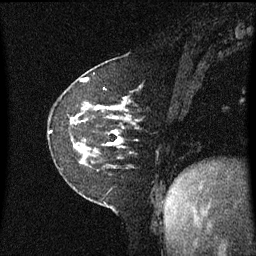
Breast MRI (dynamic contrast-enhanced), one sagittal slice; position 20 of 60 along the scan axis; dynamic contrast-enhanced series, image 2 of 3 at this slice position (ordered by acquisition); 1.5 T; TE 4.2 ms, TR 8.4 ms; 2 mm slice thickness; 256 × 256 image matrix, field of view 210 × 210 mm. Patient: female, 60 years. Case-level facts recorded for this patient, not image findings: setting: breast cancer imaged before/during neoadjuvant chemotherapy; receptor status: triple-negative.
Outlined on this slice (semi-automatically segmented with operator editing):
- analysis volume of interest (the breast-tissue region the enhancement analysis was run in; not a lesion): bounding box [x1, y1, x2, y2] px = [49, 100, 138, 169]
- tumour enhancement mask (voxels above the 70 % enhancement threshold inside the analysis volume of interest): [96, 107, 123, 145]